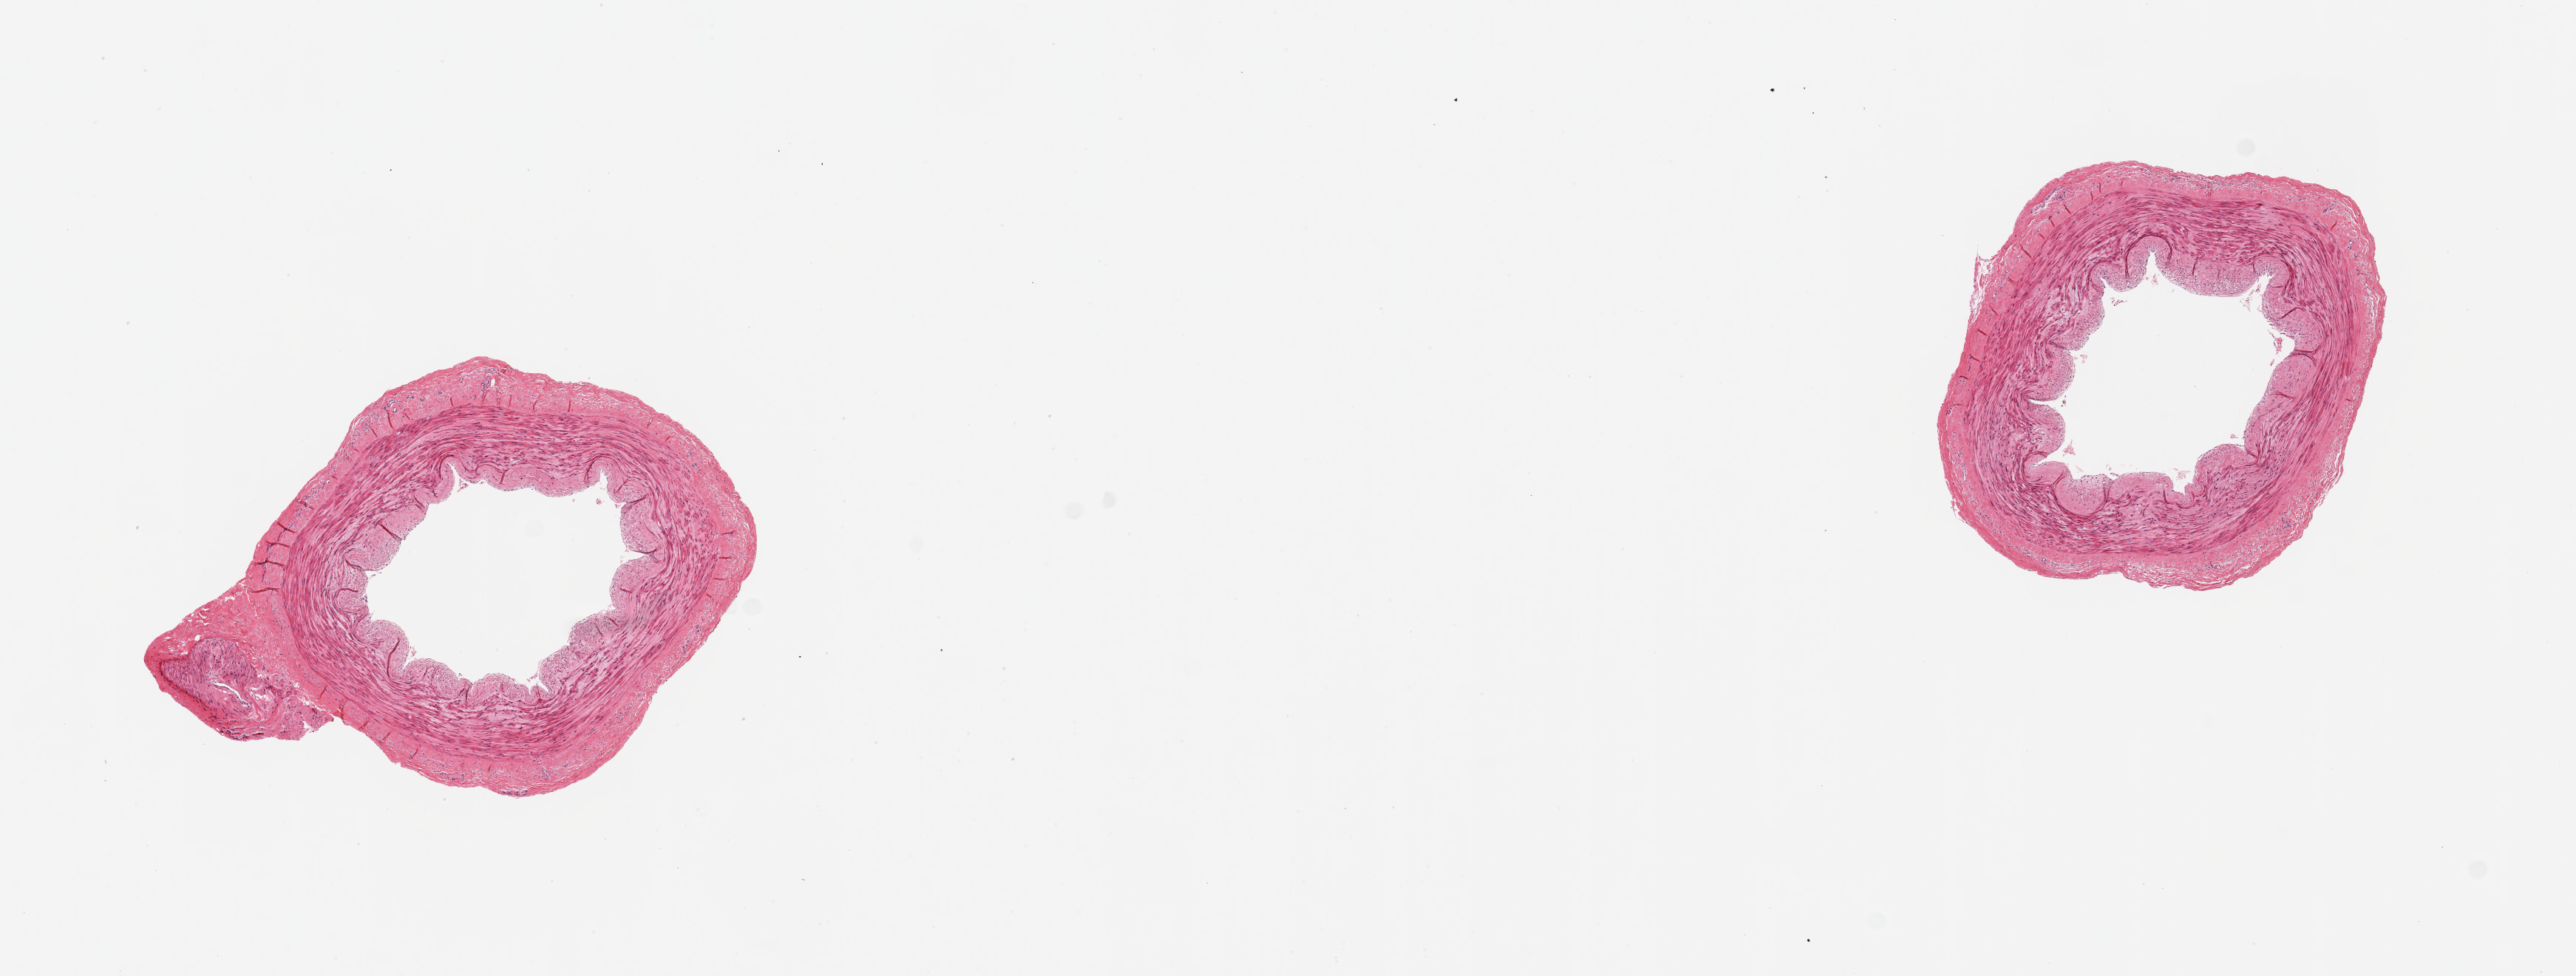
H&E whole-slide image, brightfield — whole scanned area (about 13.8 x 5.2 mm, acquisition: 20x scan) shown as a low-resolution overview; PAXgene-fixed, paraffin-embedded tissue; target tissue: tibial artery; donor tissue sample.
Review note (as recorded): 2 pieces; intimal thickening/early atherosclerosis.